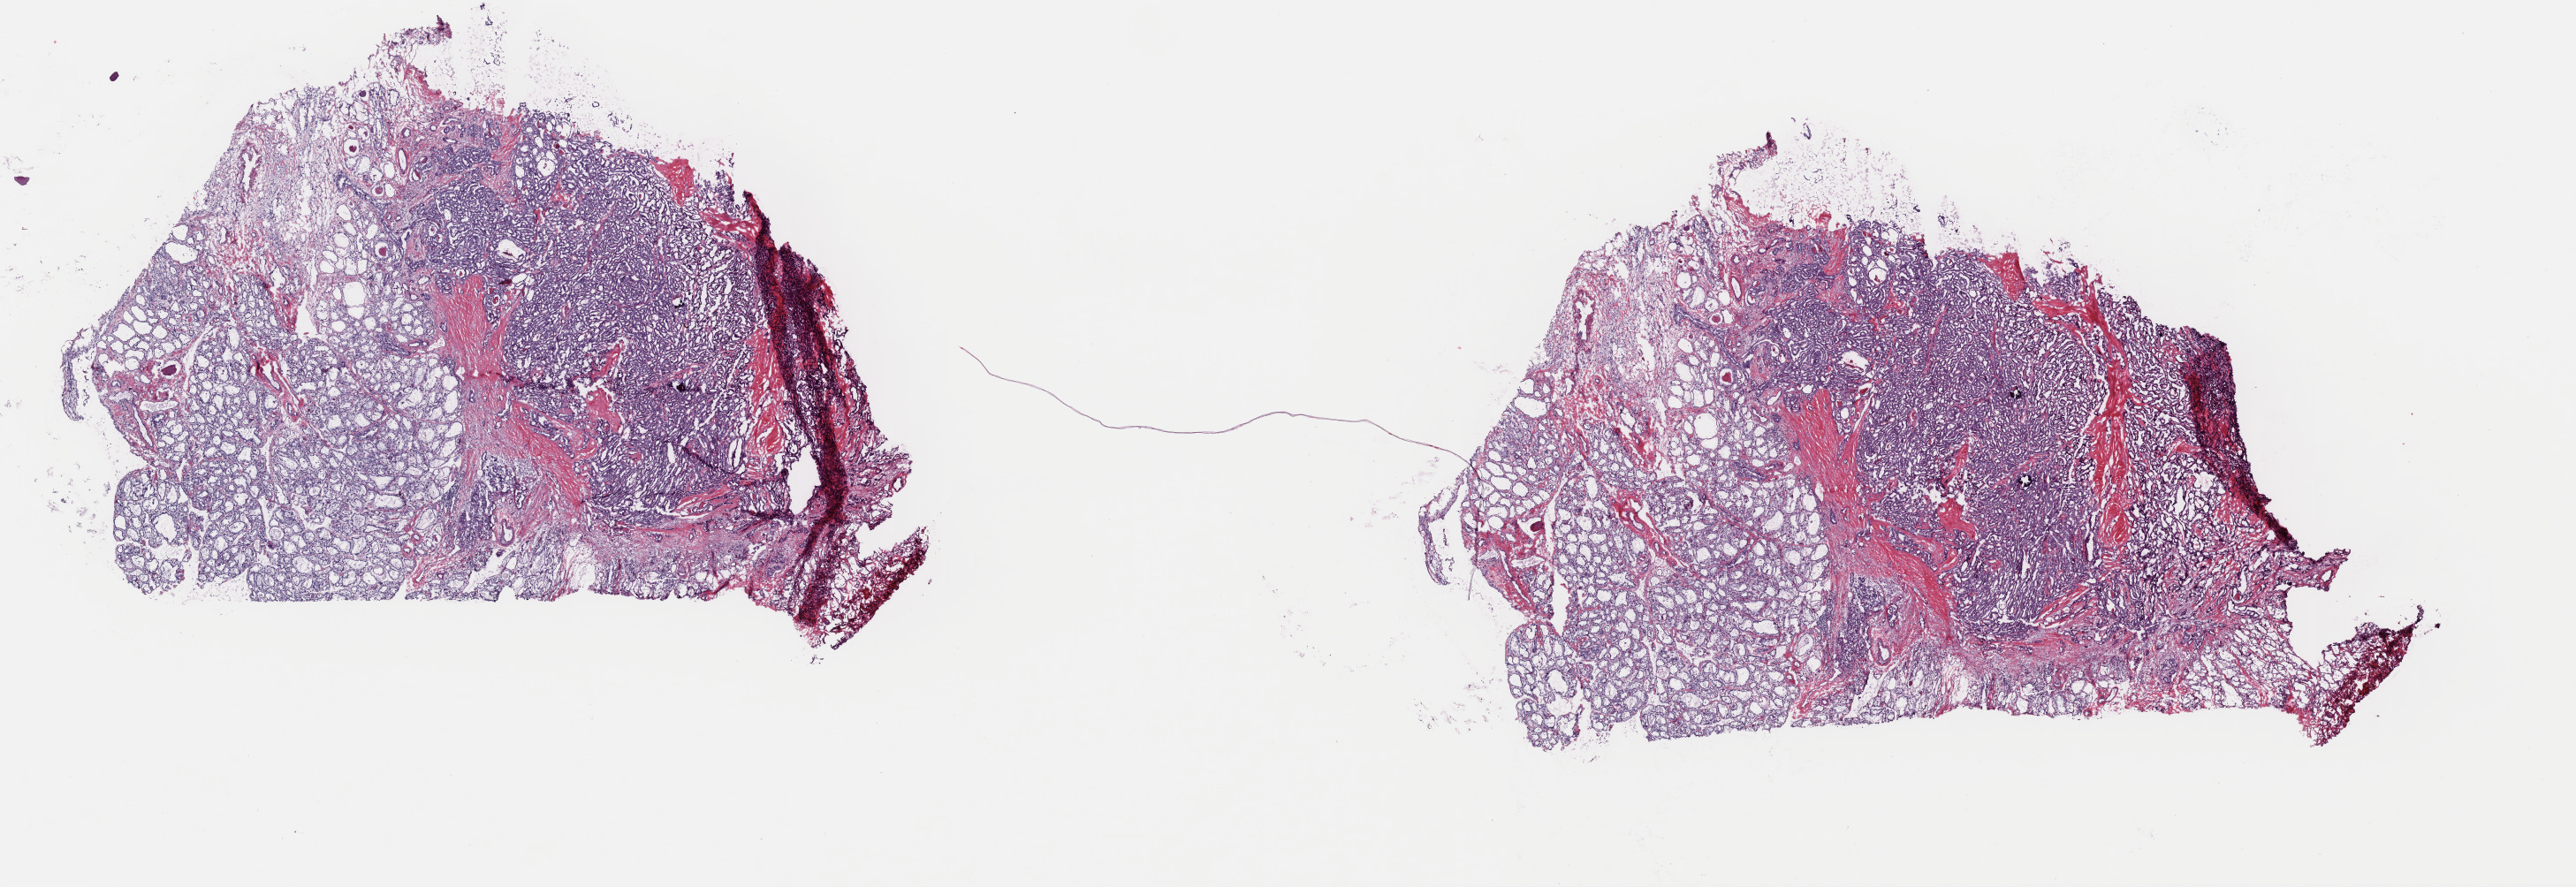
Whole-slide histology image, Hematoxylin and eosin (H&E) stained — whole scanned area (about 23.0 x 7.9 mm) shown as a low-resolution overview, frozen section from the top of the tissue portion, primary tumour sample from the thyroid. Female, age 56 years at initial diagnosis. Composition of this section per pathologist review: tumour cells 70%, tumour nuclei 70%, normal cells 20%, stromal cells 10%, necrosis 0%. Infiltration values recorded for this section: lymphocyte infiltration 0%, monocyte infiltration 0%, neutrophil infiltration 0%.
AJCC pathologic stage: I (7th edition). TNM: T1a N0 M0. Laterality: left. Histologic diagnosis: Papillary adenocarcinoma, NOS (thyroid gland).